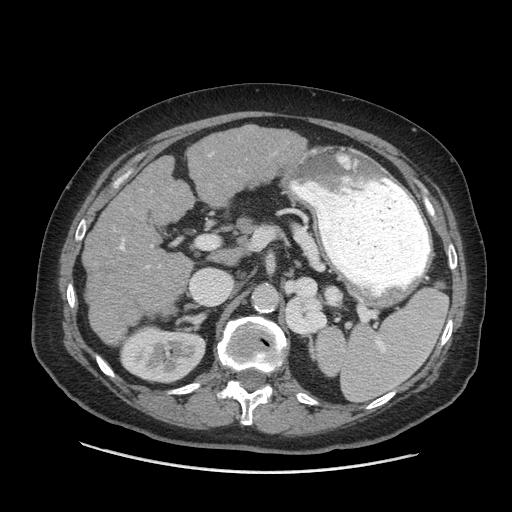
Contrast-enhanced abdominal CT (liver protocol), one axial slice. Slice 33 of 77 in the series (ordered by position). Reconstruction kernel STANDARD. 140 kVp. Soft-tissue window (W 400 / L 40 HU). 2.5 mm slice thickness. 512 × 512 image matrix. From the clinical record (not read from this slice): diagnosis: hepatocellular carcinoma (patient treated with transarterial chemoembolisation; whether this scan precedes or follows treatment is not stated here); TNM stage (as recorded): Stage-I; Child-Pugh class: A; tumour nodularity: uninodular; tumour size: 3.8 cm.
Annotated regions visible in this slice (semi-automatic segmentation, software-assisted and operator-edited):
- liver parenchyma outside the tumour (the mass and vessels are separate outlines, so this box may not span the whole liver): bounding box (x1, y1, x2, y2) in pixels: (82, 126, 317, 344)
- liver vessels: (119, 244, 149, 268)